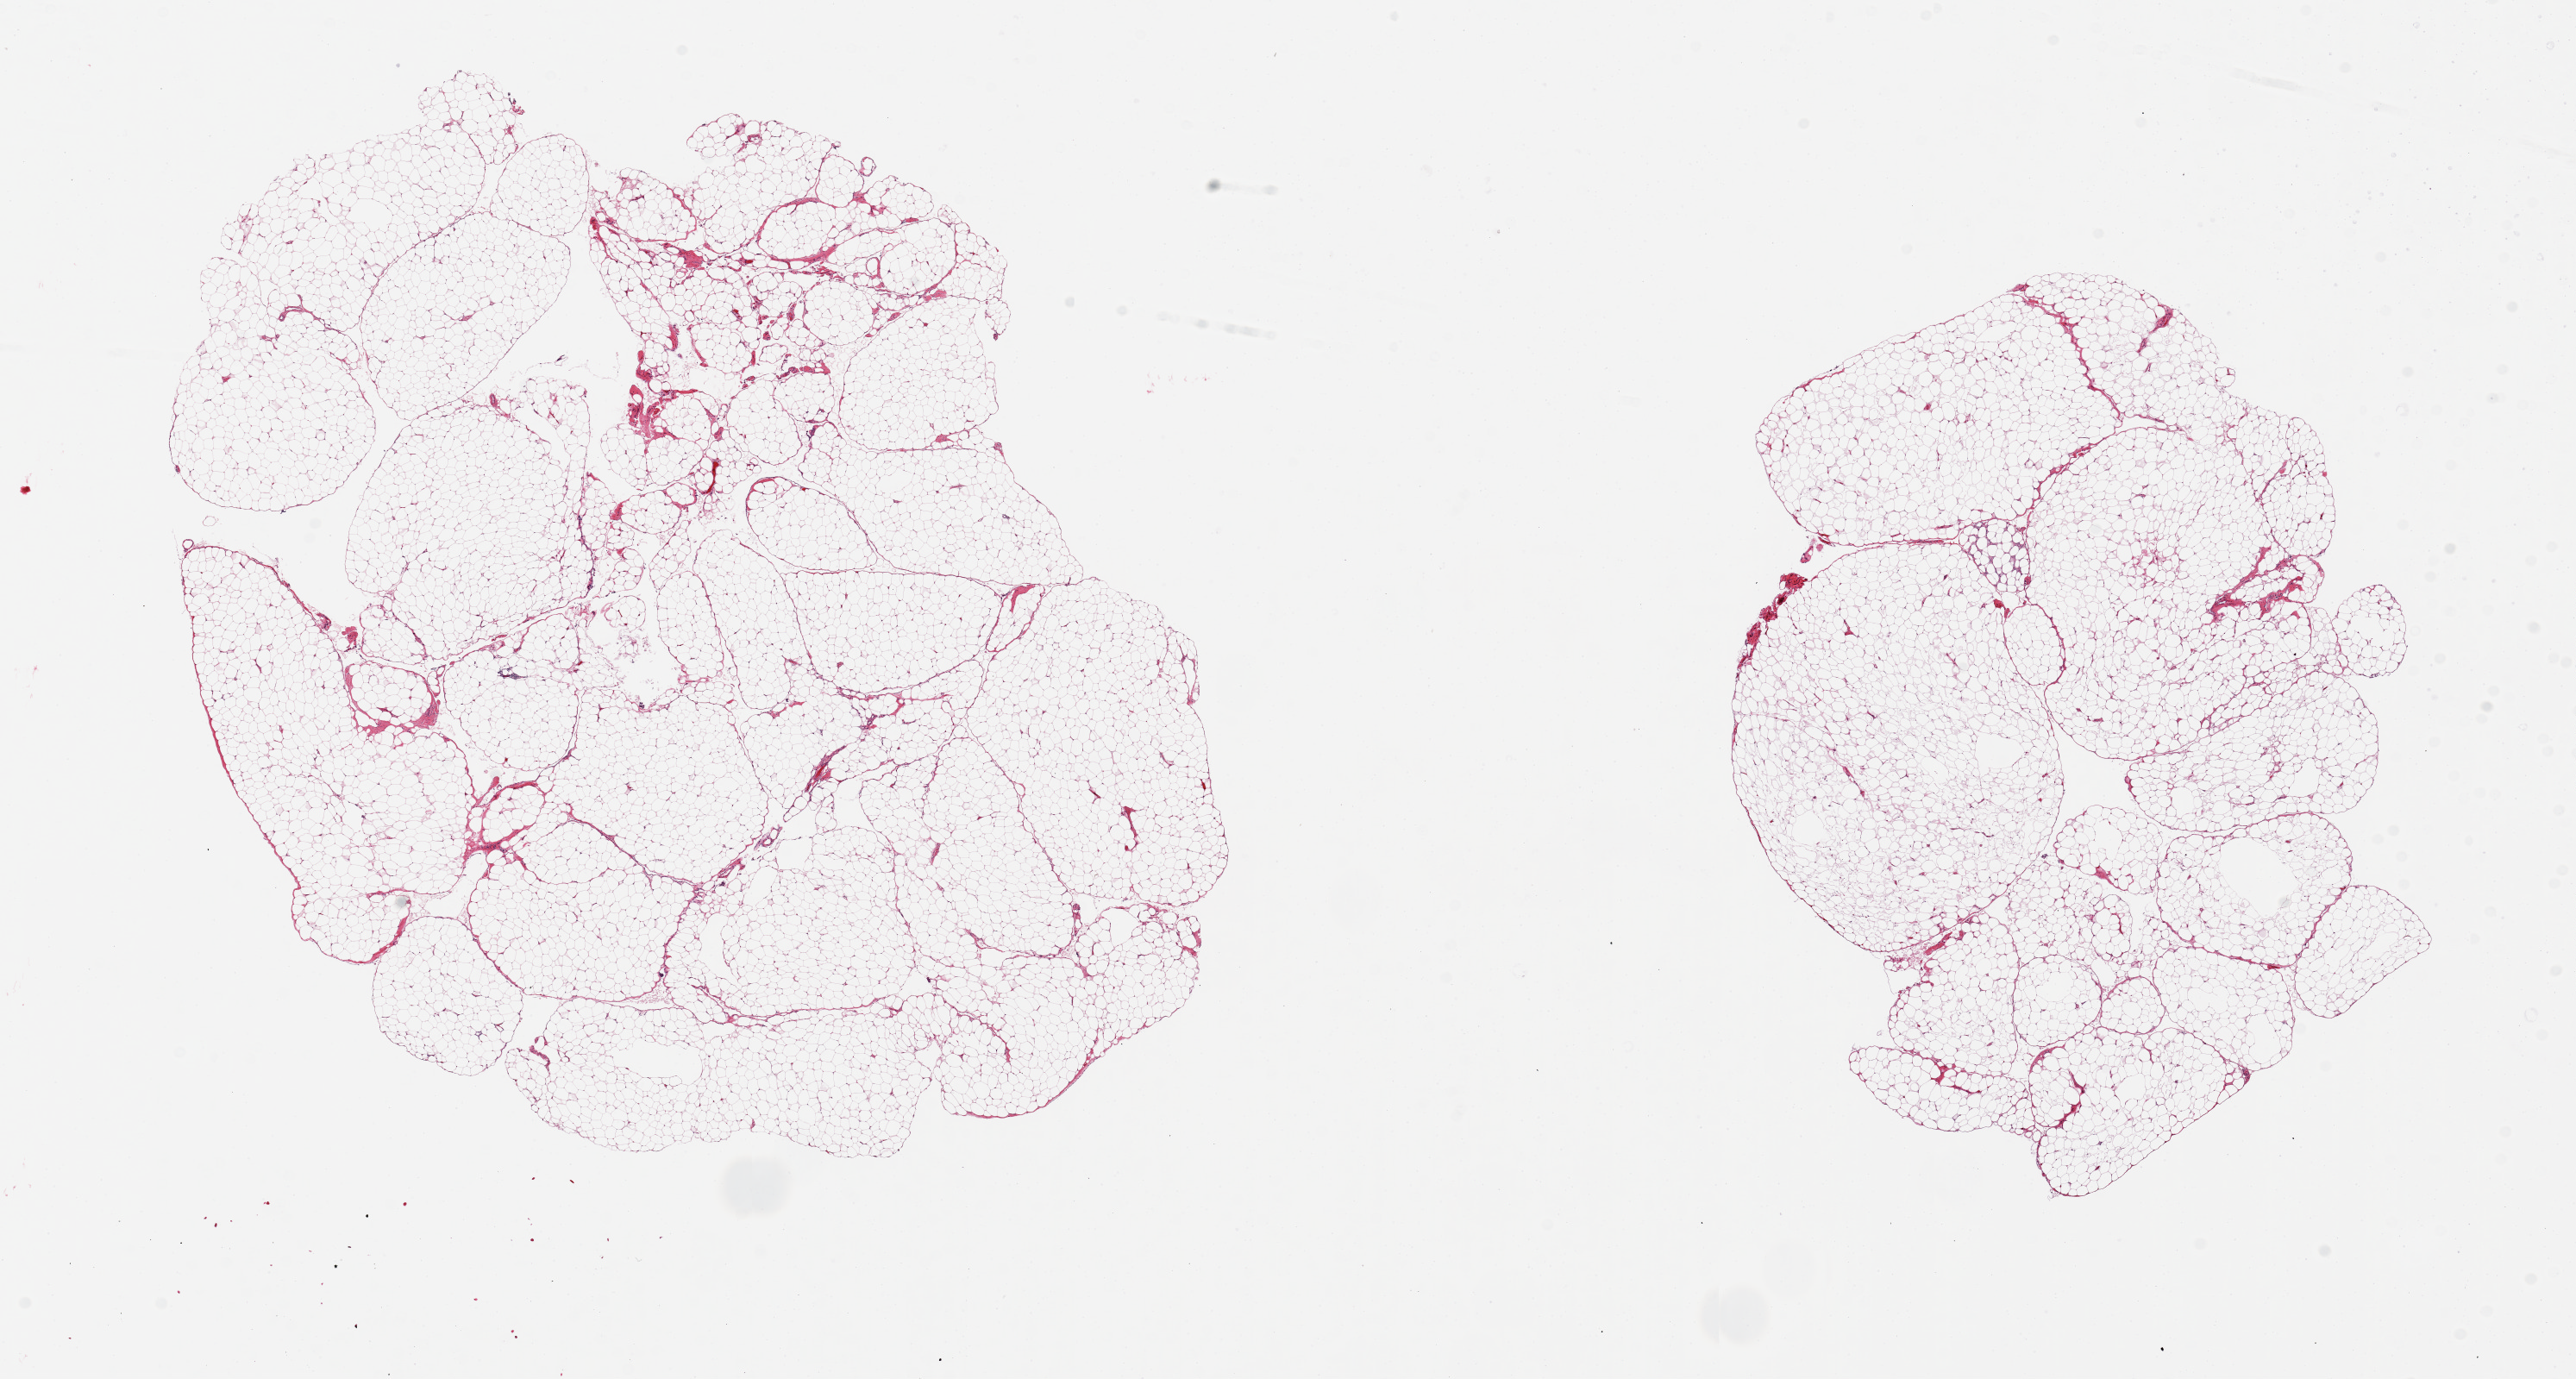
Digitized H&E-stained section, brightfield, a low-resolution overview of the entire scanned area, about 23.6 x 12.6 mm, PAXgene-fixed, paraffin-embedded tissue, sampled site (target tissue): omentum, donor tissue sample. Male donor.
* review note (as recorded): 2 pieces, 11x9 & 7x6.5mm